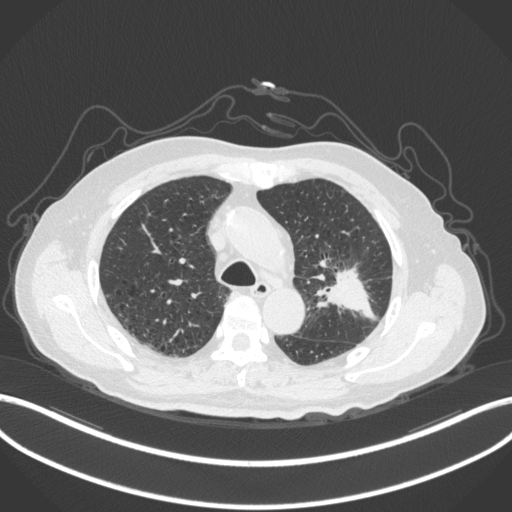
Chest CT, one axial slice. Slice 203 of 331 in the series (ordered by position). Lung window (W 1500 / L -600 HU). 512 × 512 image matrix, field of view 400 × 400 mm. Male patient, age 79 years. Case-level facts recorded for this patient, not image findings: clinical TNM (as recorded): T2a N1 M1; histopathological grade: G3.
Annotated regions visible in this slice (bounding box drawn by a radiologist):
- lung tumour (recorded histology: adenocarcinoma): bounding box (x1, y1, x2, y2) in pixels: (315, 260, 378, 322)